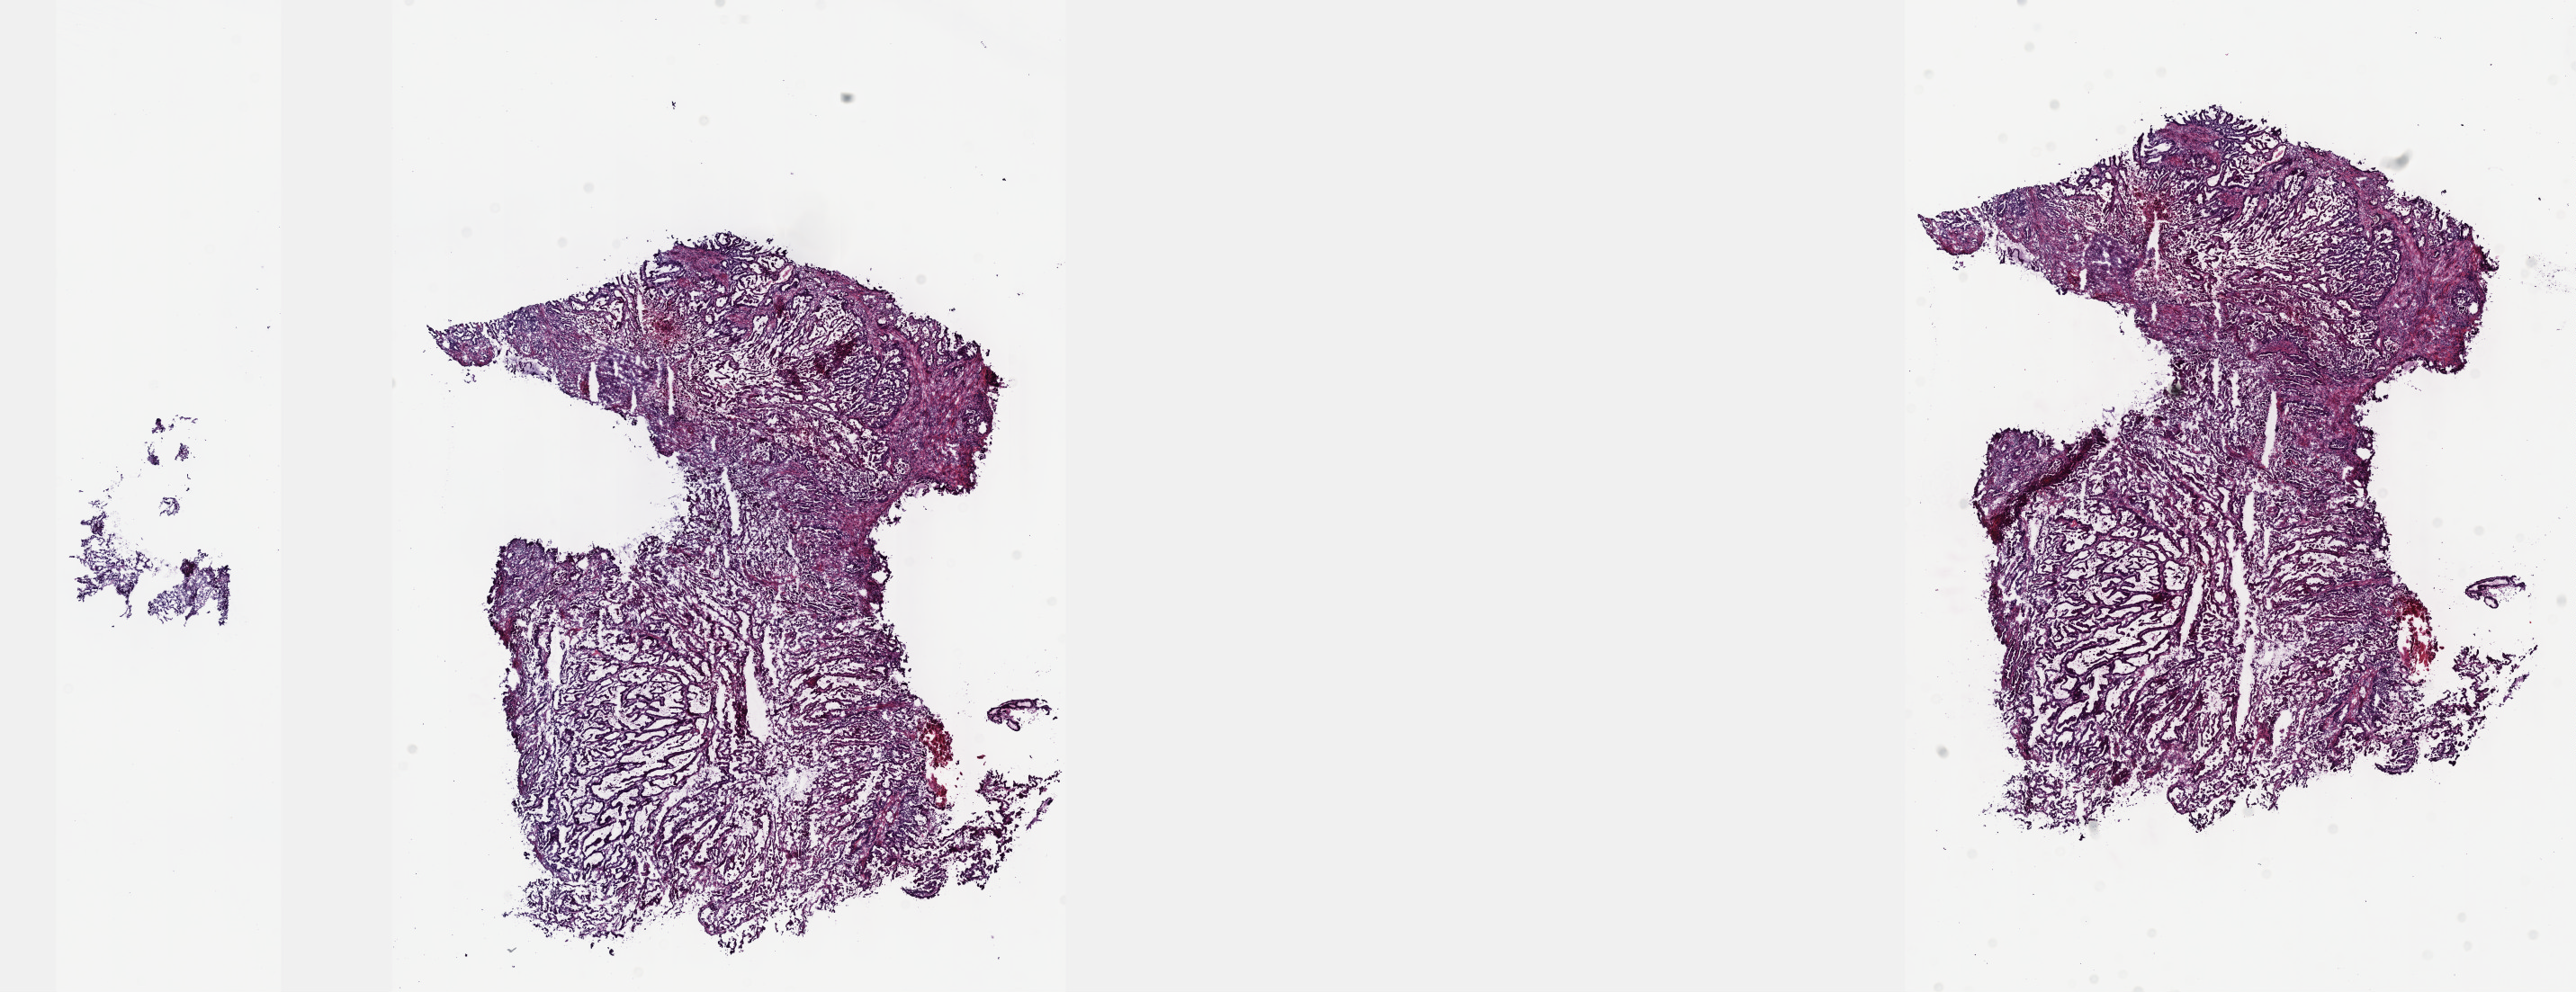
H&E-stained whole-slide image — low-resolution overview of the scanned area, about 23.1 x 8.9 mm; frozen section from the top of the tissue portion; stomach, primary tumour sample. Patient: male, age at initial diagnosis 67 years. Histologic grade: G2 (moderately differentiated). Composition of this section per pathologist review: tumour cells 75%, tumour nuclei 75%, normal cells 0%, stromal cells 23%, necrosis 2%. Infiltration values recorded for this section: lymphocyte infiltration 4%, monocyte infiltration 2%, neutrophil infiltration 3%.
- AJCC pathologic stage: IB (6th edition)
- lymph nodes positive (case pathology): 0 of 28 examined
- diagnosis: Tubular adenocarcinoma